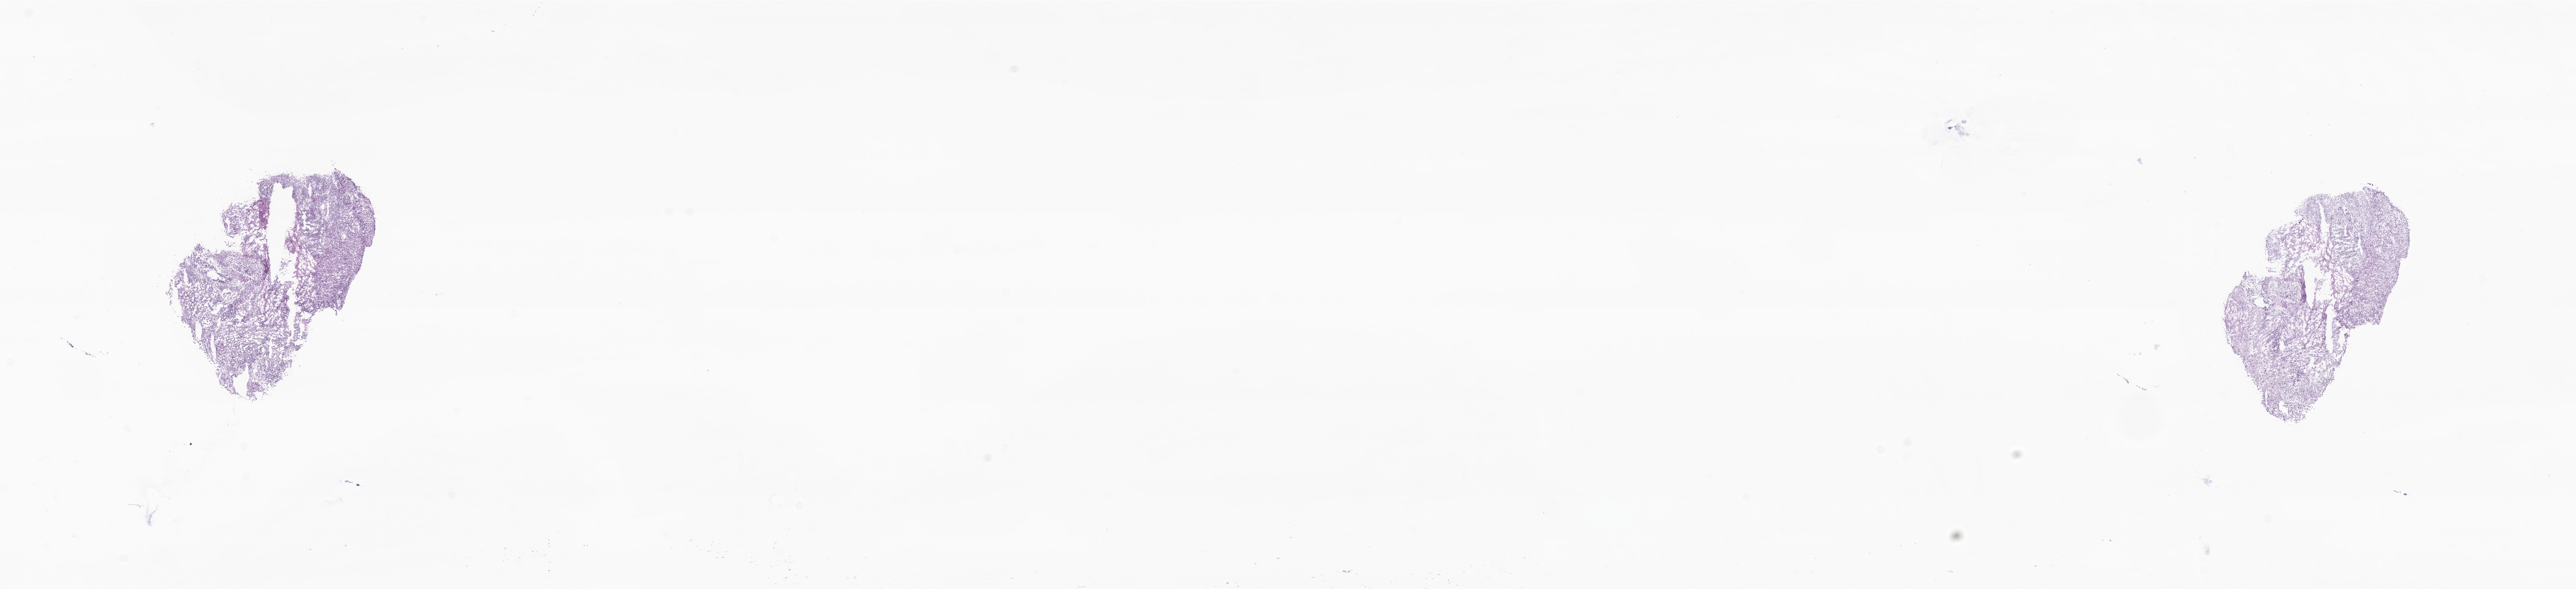
Digitized haematoxylin and eosin-stained section of tumor tissue from the brain stem — a low-resolution overview of the entire scanned area, about 29.1 x 6.7 mm, frozen section. Patient: male, age 543 days (about 1.5 years).
- recorded diagnosis: Medulloblastoma, NOS